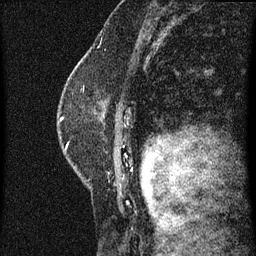
Breast MRI (dynamic contrast-enhanced), one sagittal slice; slice 44 of 60 in the series (ordered by position); dynamic contrast-enhanced series, image 2 of 3 at this slice position (ordered by acquisition); 1.5 T; TE 4.2 ms, TR 8 ms; 2 mm slice thickness; 256 × 256 image matrix, field of view 180 × 180 mm. Patient: female, 47 years.
Structures marked on this image (semi-automatic segmentation, software-assisted and operator-edited):
- analysis volume of interest (the breast-tissue region the enhancement analysis was run in; not a lesion): bounding box (x1, y1, x2, y2) in pixels: (58, 80, 133, 187)
- tumour enhancement mask (voxels above the 70 % enhancement threshold inside the analysis volume of interest): (61, 118, 63, 121)